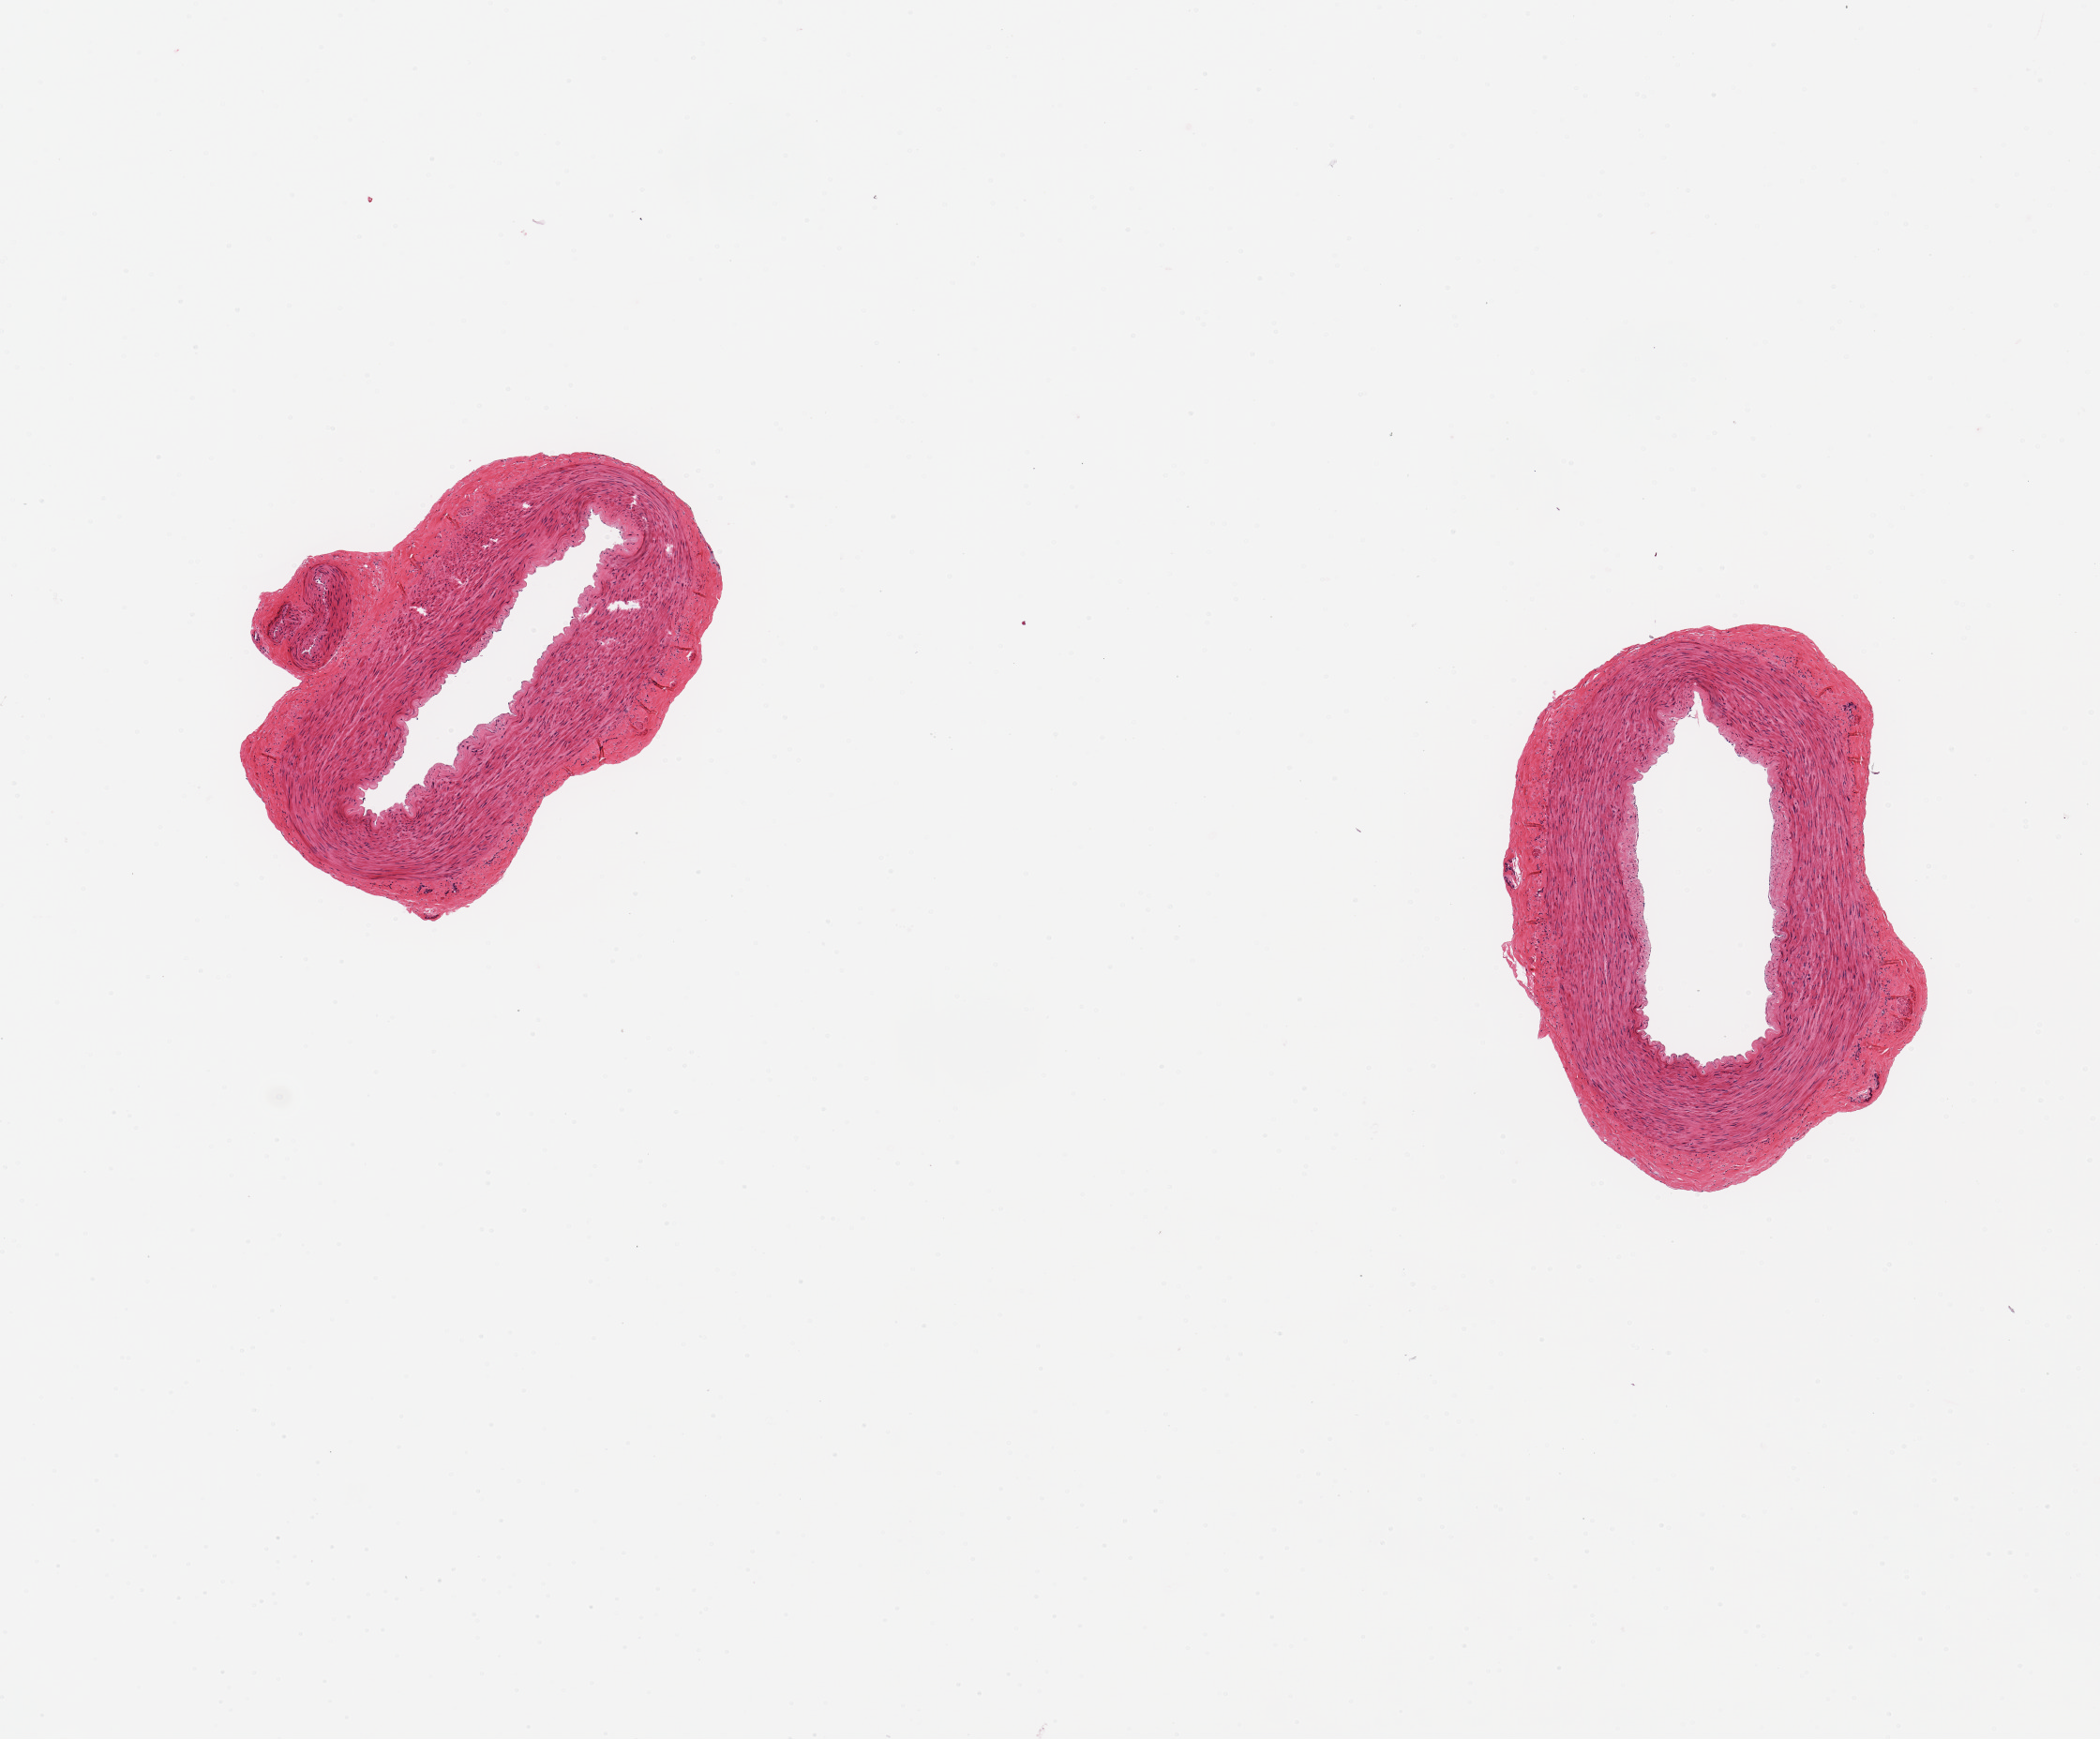
Hematoxylin and eosin (H&E) whole-slide image — whole scanned area (about 8.9 x 7.3 mm, acquisition: 20x scan) shown as a low-resolution overview, PAXgene-fixed, paraffin-embedded tissue, target tissue: tibial artery, tissue donor sample. Donor sex: male.
Review note (as recorded): 2 pieces, ~2x1.3 mm. Minimal intimal sclerosis; no adherent fat (good dissection); focal tissue tears (probably not due to fixation).